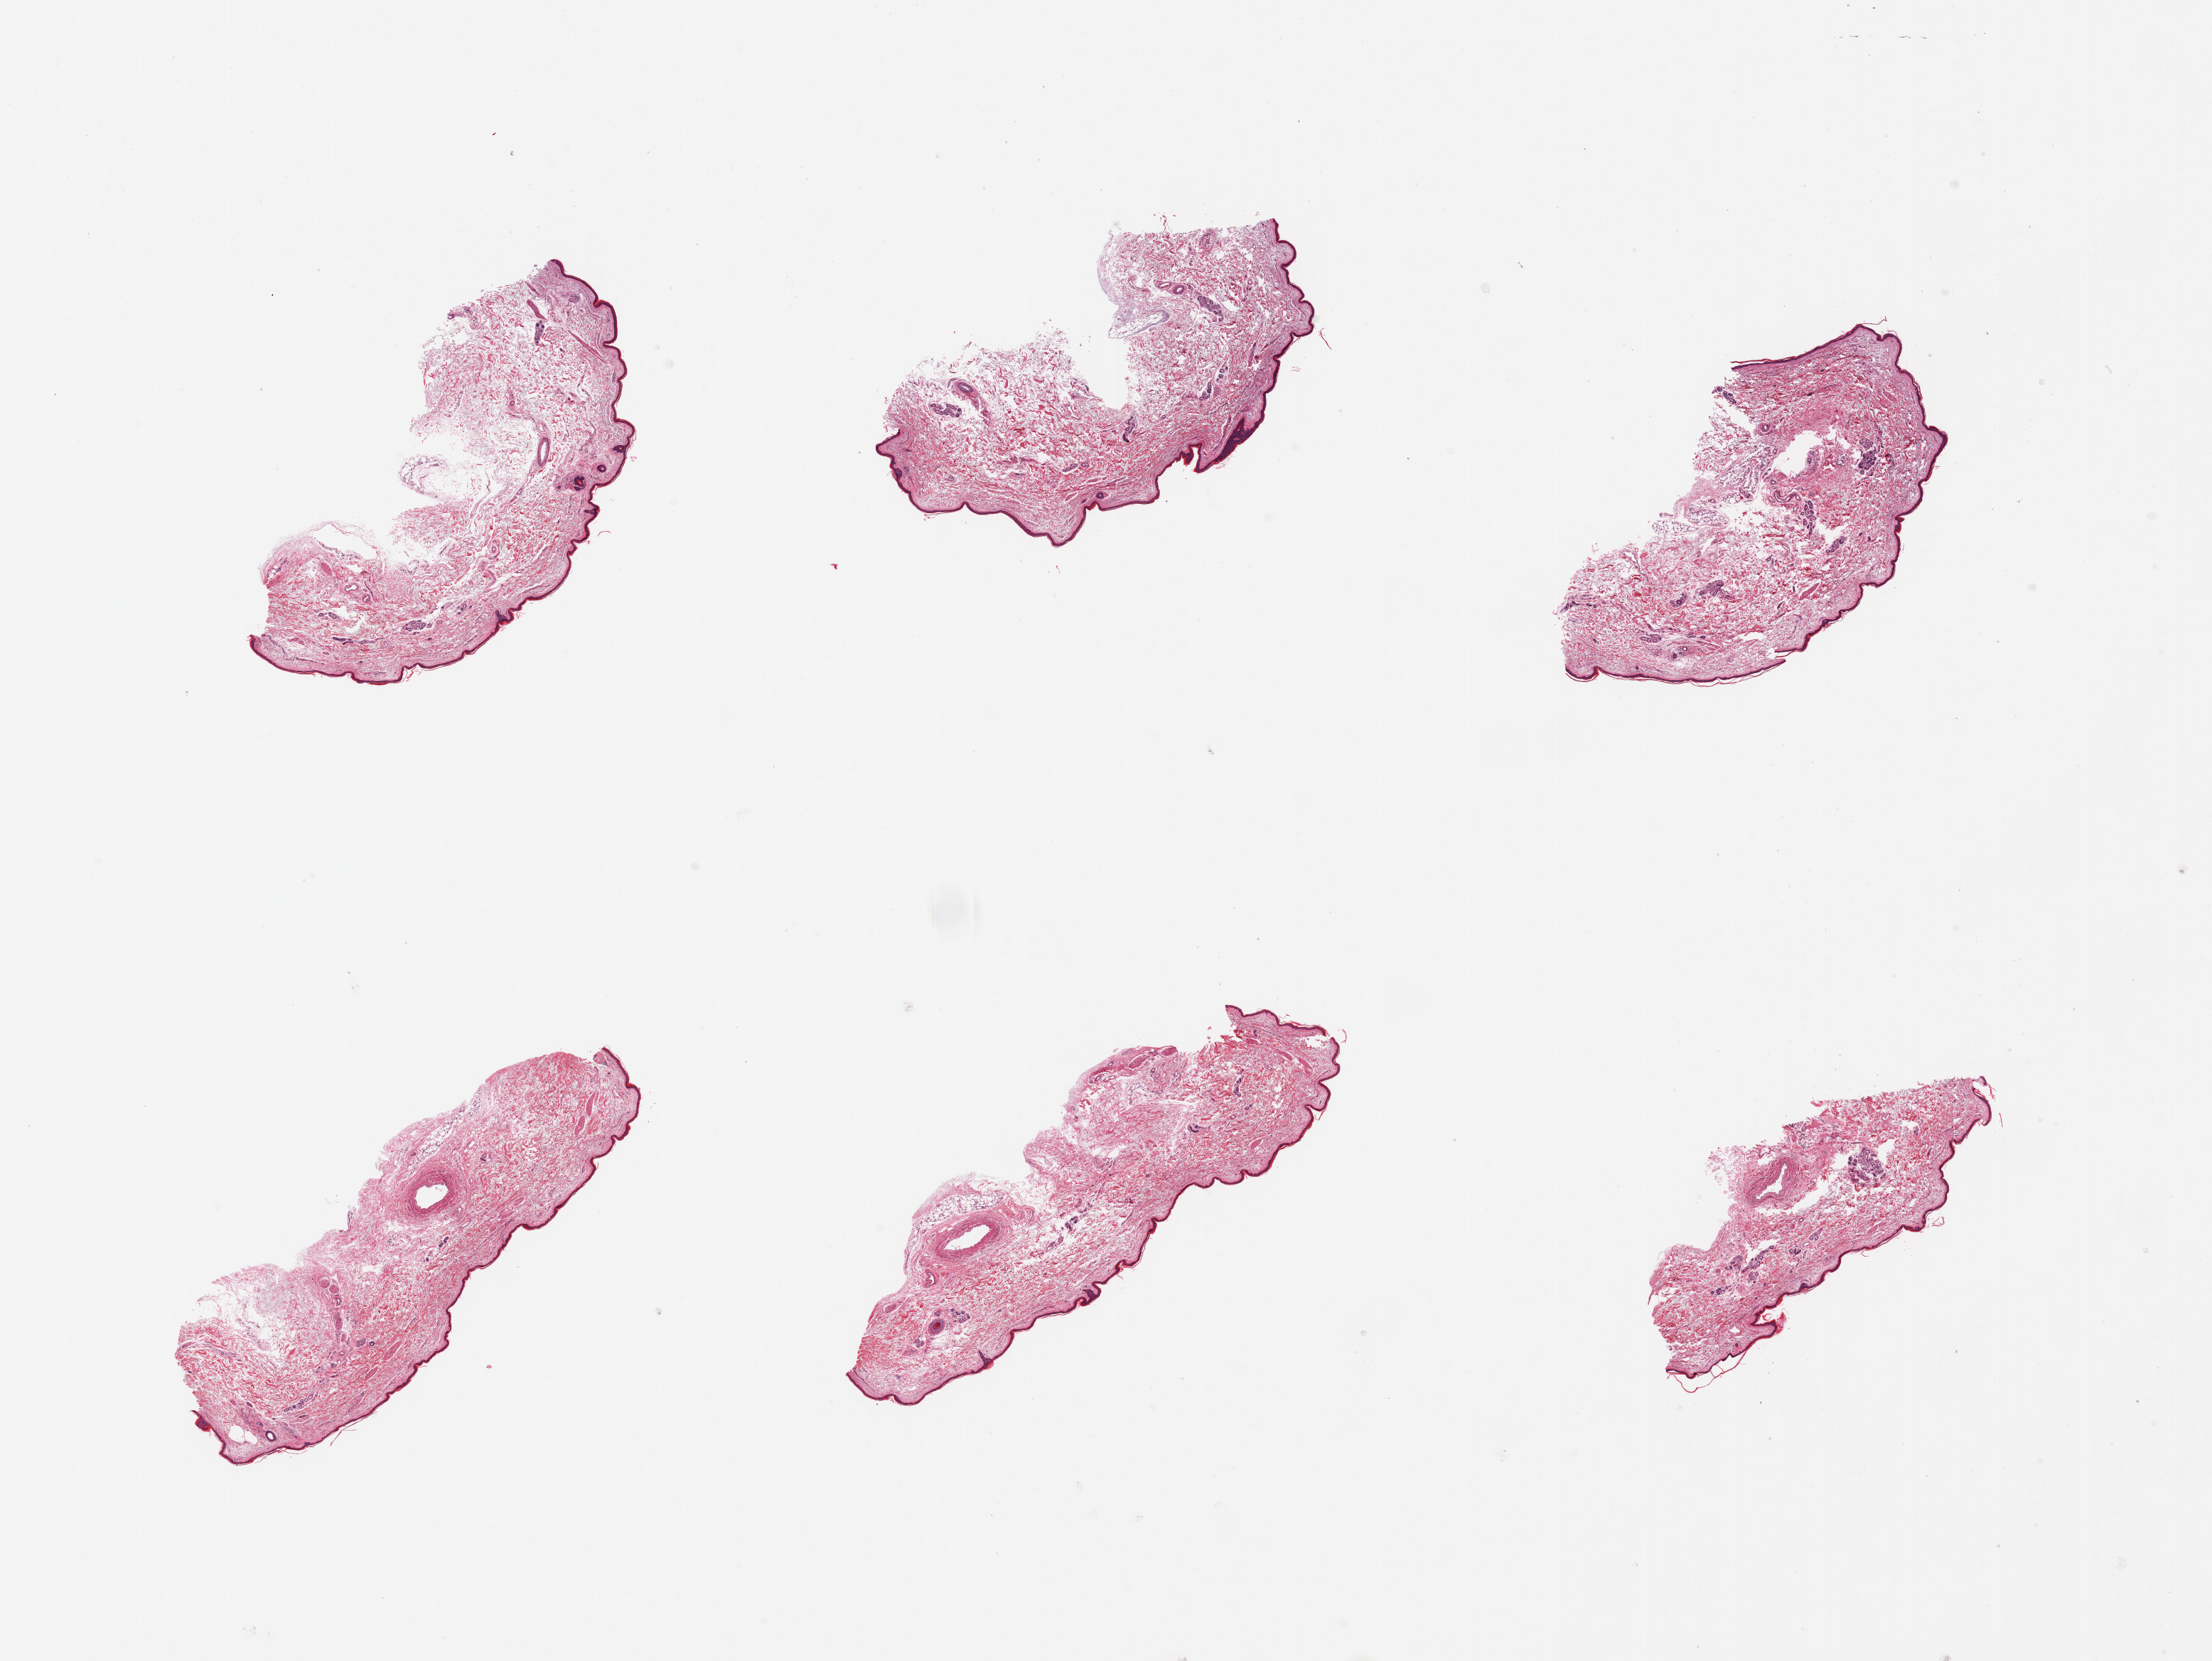
Haematoxylin and eosin whole-slide image — shown as a low-resolution overview of the whole scanned area (about 24.6 x 18.5 mm). PAXgene-fixed, paraffin-embedded tissue. Section of skin of lower leg (target tissue). Tissue donor sample. Donor sex: male.
Review note (as recorded): 6 pieces; atrophic, thin epidermis; edematous dermis; well trimmed.